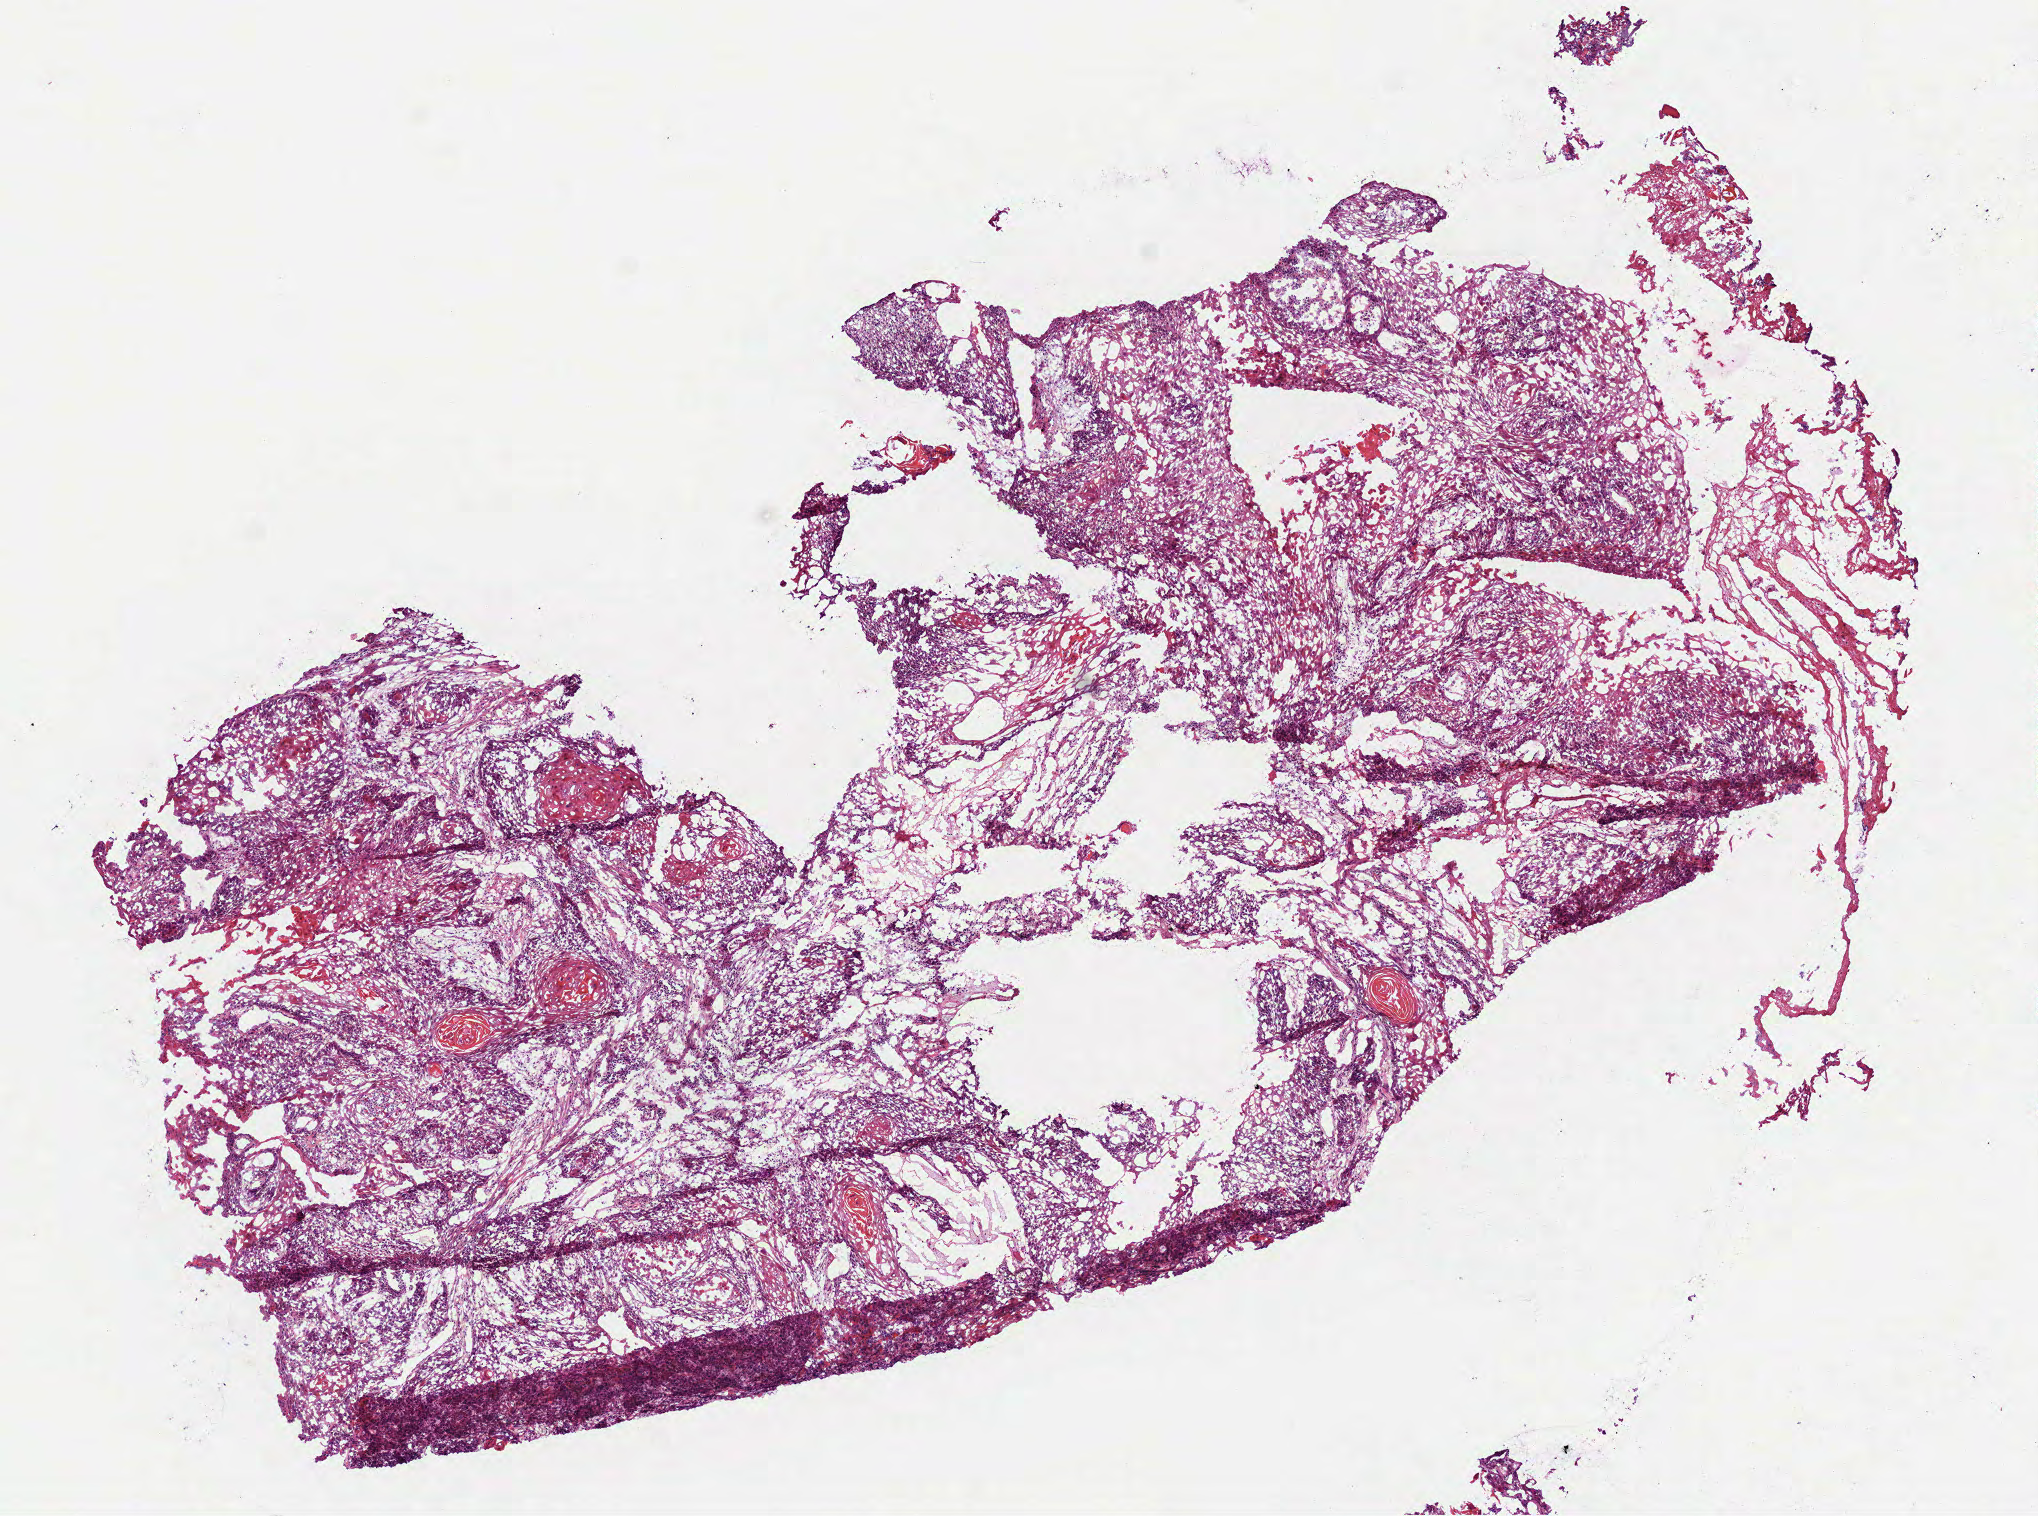
Hematoxylin and eosin (H&E) stained whole-slide image — shown as a low-resolution overview of the whole scanned area (about 8.2 x 6.1 mm). Frozen section from the bottom of the tissue portion. Head and neck, primary tumour sample. Male patient; age at initial diagnosis 62 years. Histologic grade: G2 (moderately differentiated). Composition of this section per pathologist review: tumour cells 70%, tumour nuclei 75%, normal cells 0%, stromal cells 30%, necrosis 0%.
- AJCC pathologic stage: IVA (7th edition)
- diagnosis: Squamous cell carcinoma, NOS (larynx, NOS)